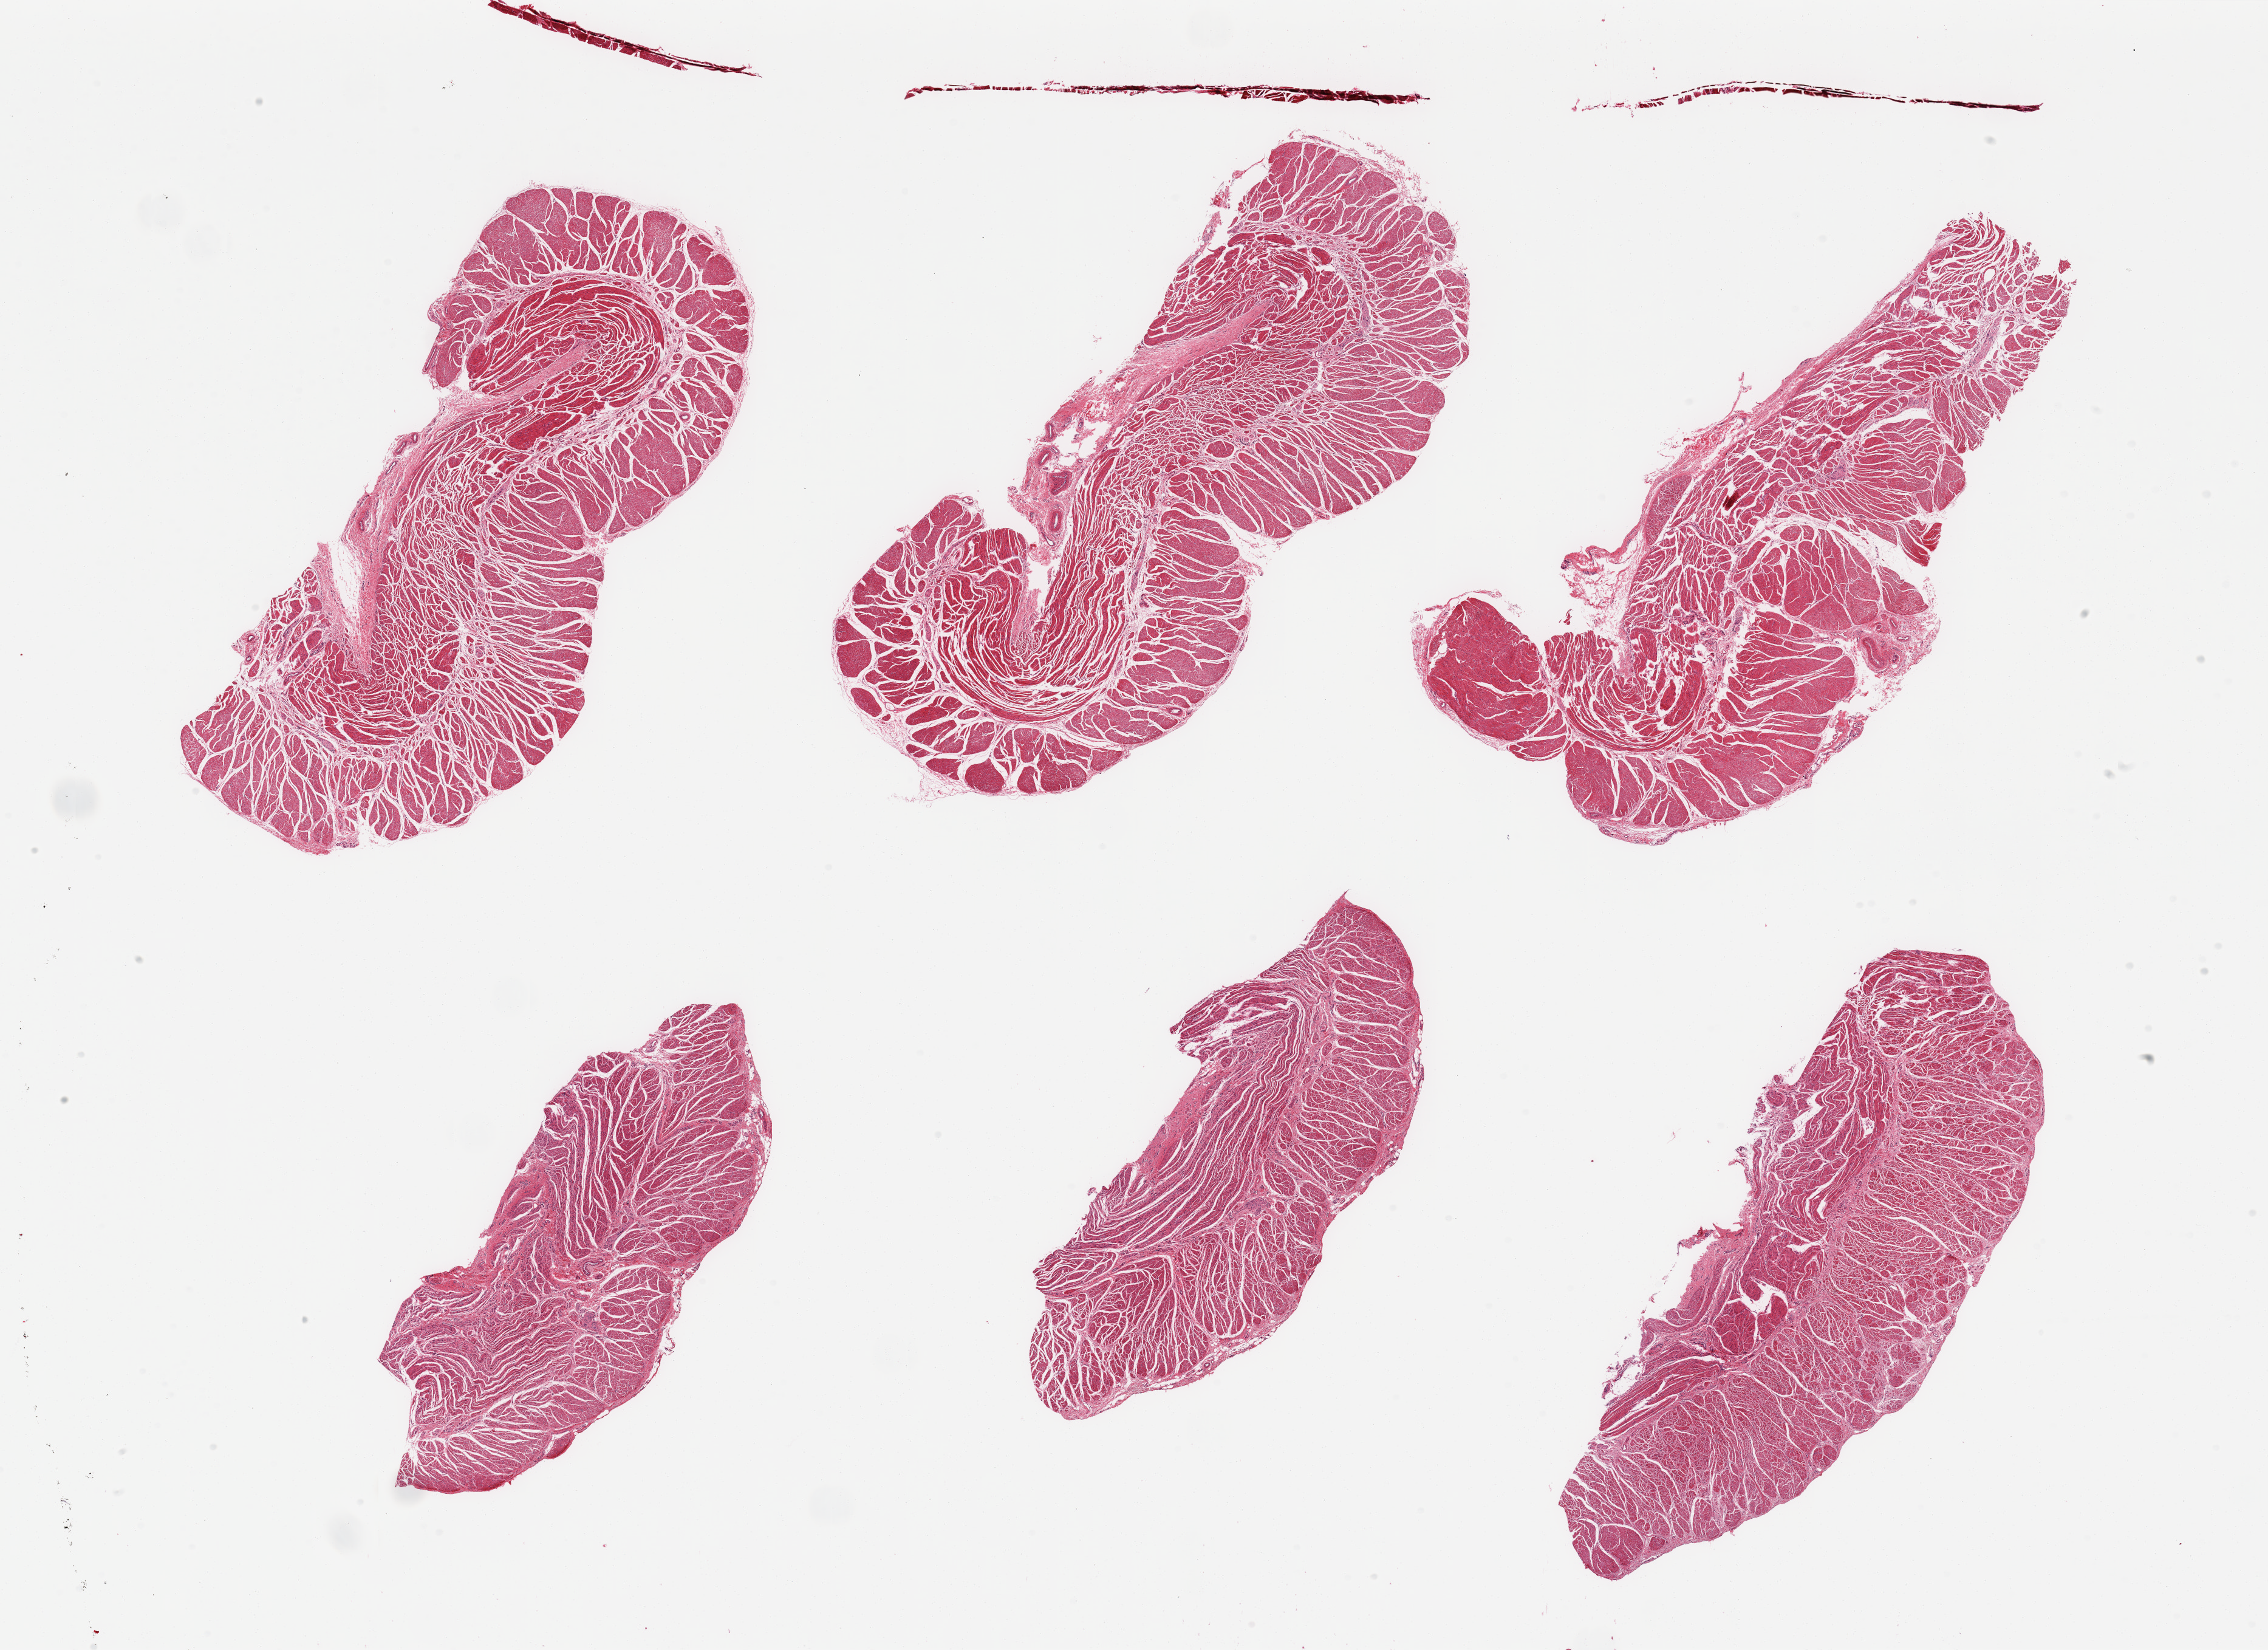
Whole-slide image, H&E stain, brightfield, whole scanned area (about 29.5 x 21.5 mm, from a 20x scan) shown as a low-resolution overview. PAXgene-fixed paraffin-embedded (PFPE) section. Sampled site (target tissue): gastroesophageal junction. Tissue donor sample. Female donor.
Reviewer comment on this tissue sample: 6 pieces; target muscularis.